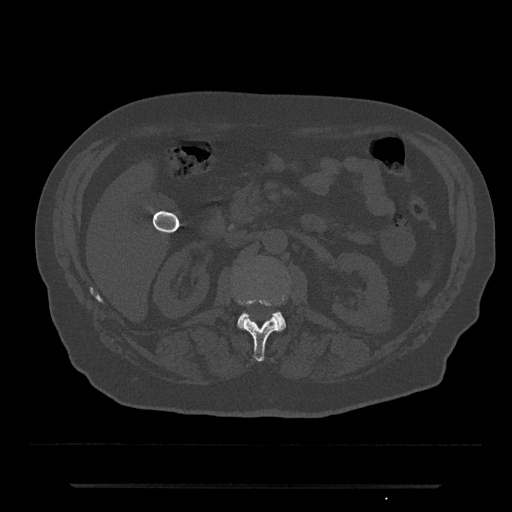
CT including the spine, one axial slice; slice 511 of 797 in the series (ordered by position); 120 kVp; bone window (W 1800 / L 400 HU); 0.5 mm slice thickness; 512 × 512 image matrix. Patient: male, 80 years. From the clinical record (not read from this slice): primary cancer: prostate; vertebrae with lytic lesions (as recorded): L1, T11.
Annotated regions visible in this slice (semi-automatic segmentation, software-assisted and operator-edited):
- L1 vertebra: bounding box <239,300,280,362> (left, top, right, bottom; pixels)
- L2 vertebra: <237,312,286,332>